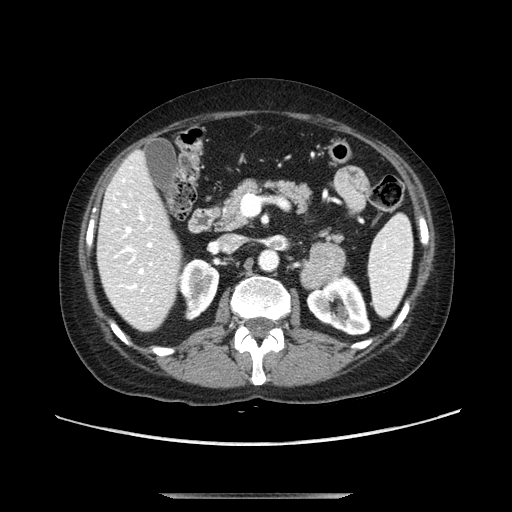
Contrast-enhanced abdominal CT, one axial slice. Position 55 of 107 along the scan axis. Soft-tissue window (W 400 / L 40 HU). 2.5 mm slice thickness. 512 × 512 image matrix, field of view 380 × 380 mm. Female patient. From the clinical record (not read from this slice): diagnosis: adrenocortical carcinoma; tumour side: left adrenal; tumour size at pathology: 7.5 cm; Ki-67 index: 9 %; stage (as recorded): 3.
Annotated regions visible in this slice (semi-automatic segmentation, software-assisted and operator-edited):
- mass: bounding box (x1, y1, x2, y2) in pixels: (300, 243, 345, 288)